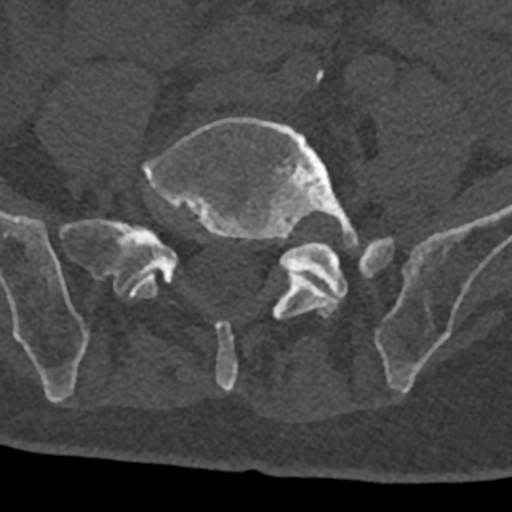
CT including the spine, one axial slice; position 181 of 797 along the scan axis; reconstruction kernel Br40s/3; bone window (W 1800 / L 400 HU); 512 × 512 image matrix, field of view 160 × 160 mm. Male patient, age 74 years. Case-level facts recorded for this patient, not image findings: primary cancer: renal; vertebrae with lytic lesions (as recorded): T10, L1, L2, L3, L4, L5.
Outlined on this slice (semi-automatic segmentation, software-assisted and operator-edited):
- L4 vertebra: bounding box <315,70,323,83> (left, top, right, bottom; pixels)
- L5 vertebra: <129,117,359,392>